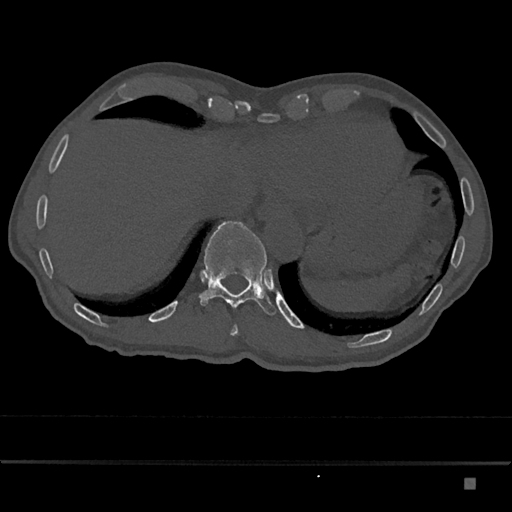
CT including the spine, one axial slice; slice 685 of 797 in the series (ordered by position); reconstruction kernel Br40s/3; 120 kVp; bone window (W 1800 / L 400 HU); 512 × 512 image matrix. Patient: male, 72 years. Case-level facts recorded for this patient, not image findings: primary cancer: prostate.
Structures marked on this image (semi-automatic segmentation, software-assisted and operator-edited):
- T10 vertebra: box from (x=231, y=324) to (x=238, y=336) px
- T11 vertebra: (x=199, y=221)–(x=276, y=316)